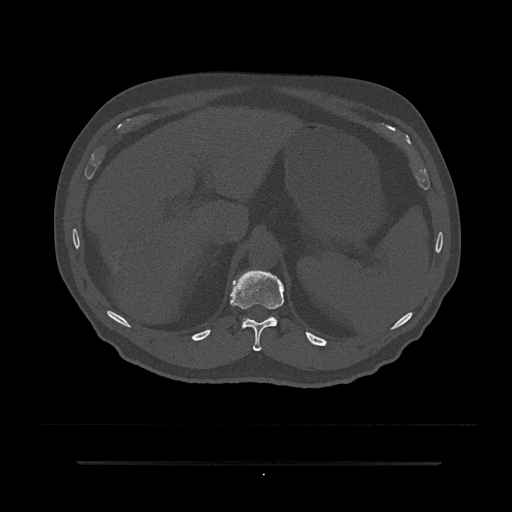
CT including the spine, one axial slice. Slice 253 of 797 in the series (ordered by position). Reconstruction kernel Br40s/3. 120 kVp. Bone window (W 1800 / L 400 HU). 0.5 mm slice thickness. 512 × 512 image matrix, field of view 464 × 464 mm. Patient: male, 59 years. Case-level facts recorded for this patient, not image findings: primary cancer: bile ducts; vertebrae with lytic lesions (as recorded): T10.
Outlined on this slice (semi-automatically segmented with operator editing):
- T11 vertebra: bounding box [x1, y1, x2, y2] px = [230, 270, 284, 352]
- T12 vertebra: [242, 316, 277, 328]